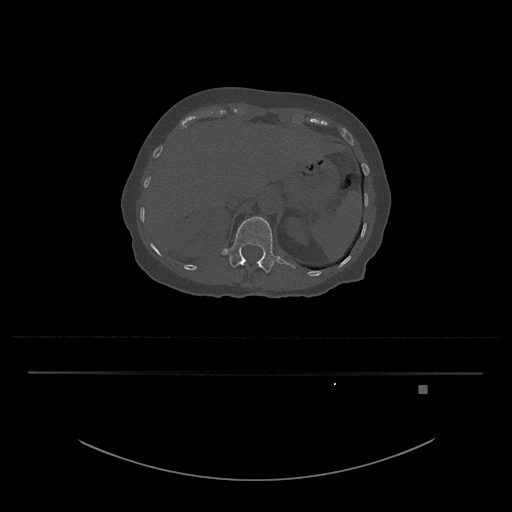
CT including the spine, one axial slice; 120 kVp; bone window (W 1800 / L 400 HU); 0.5 mm slice thickness; 512 × 512 image matrix, field of view 500 × 500 mm. Patient: female, 57 years. From the clinical record (not read from this slice): primary cancer: cervical.
Outlined on this slice (semi-automatic segmentation, software-assisted and operator-edited):
- L1 vertebra: bounding box [x1, y1, x2, y2] px = [221, 216, 295, 273]